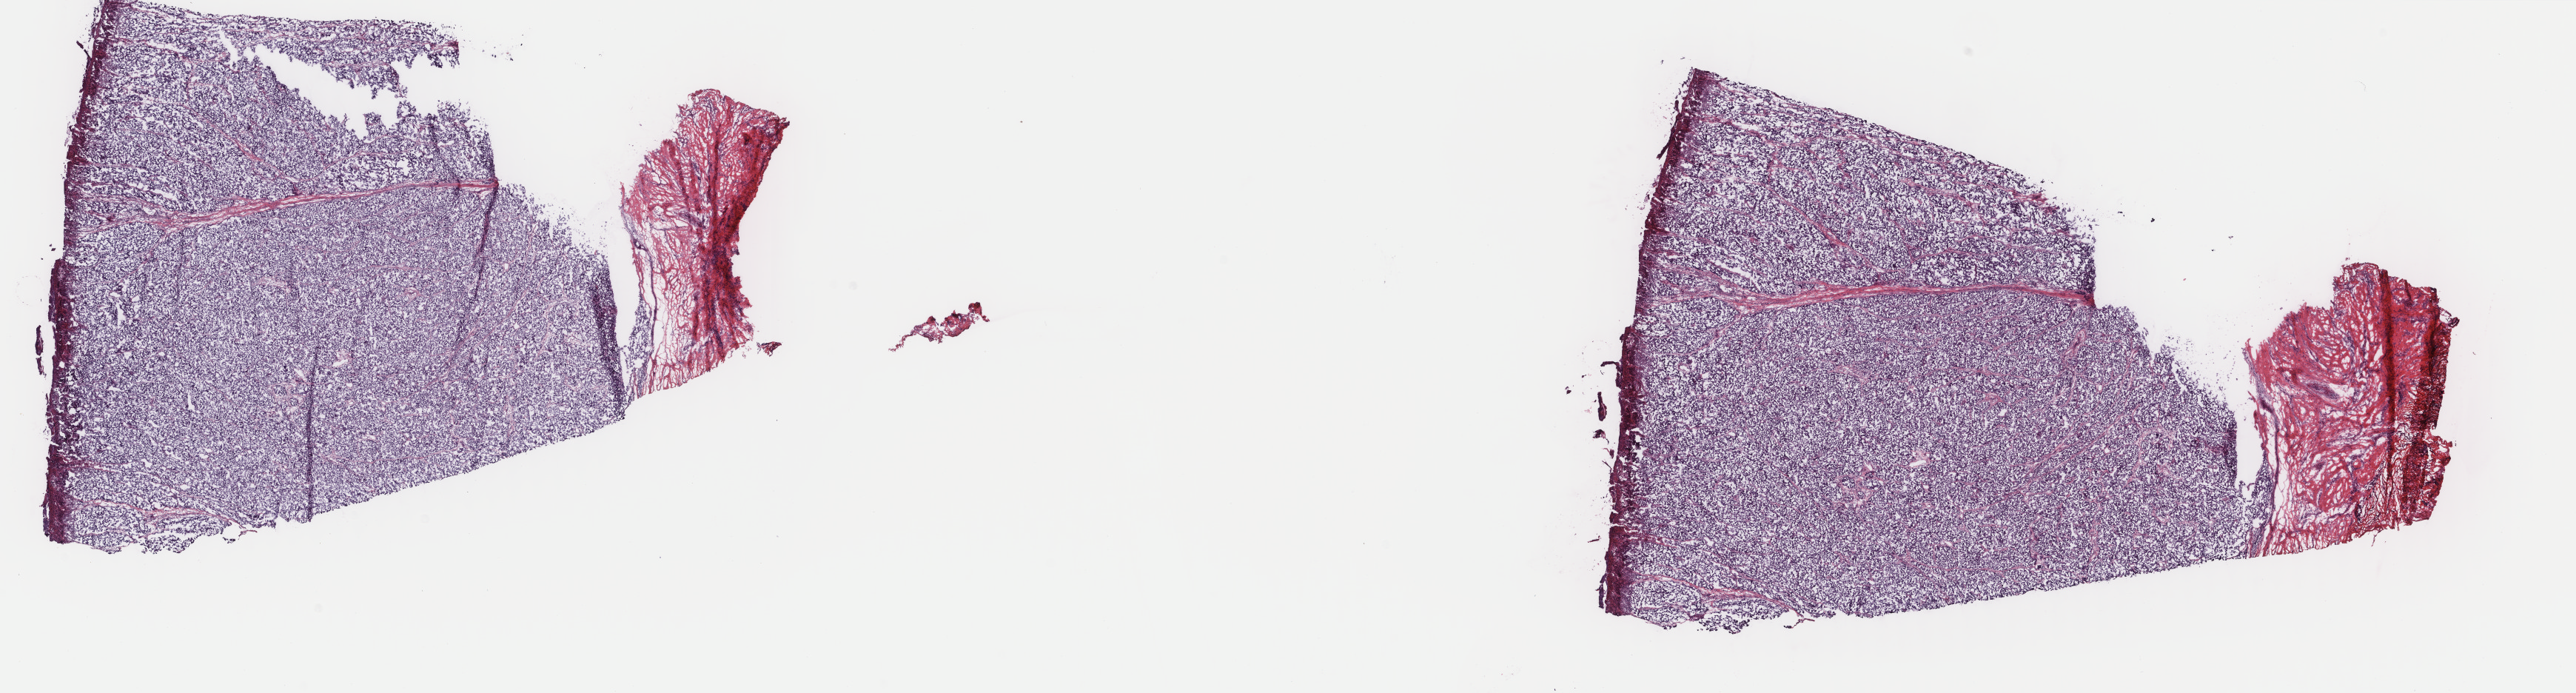
Digitized H&E-stained tissue section (whole slide), low-resolution overview of the scanned area, about 27.6 x 7.4 mm (slide scanned at 40x); frozen section from the top of the tissue portion; sample: primary tumour, skin. Male, age 34 years at initial diagnosis. Slide review estimates, as recorded: tumour cells 90%, tumour nuclei 90%, normal cells 10%, stromal cells 0%, necrosis 0%. Infiltration values recorded for this section: lymphocyte infiltration 1%, monocyte infiltration 0%, neutrophil infiltration 0%.
AJCC pathologic stage: IIC (7th edition). Histologic diagnosis: Nodular melanoma.